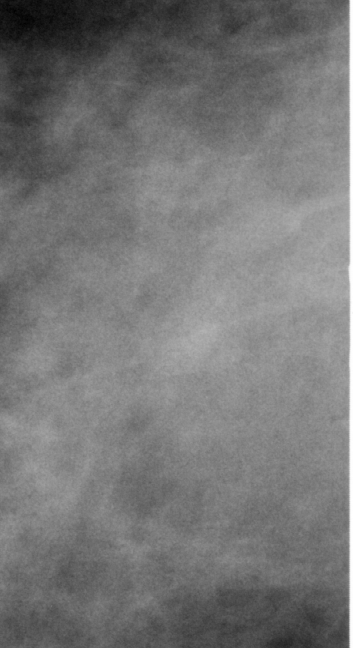
Crop from a digitized film mammogram around one marked abnormality, right breast, MLO view.
Mass, shape oval, margins obscured; BI-RADS assessment category 3; subtlety rating 4 on a 1 (subtle) to 5 (obvious) scale; pathology result (as recorded, not read from the image): benign.